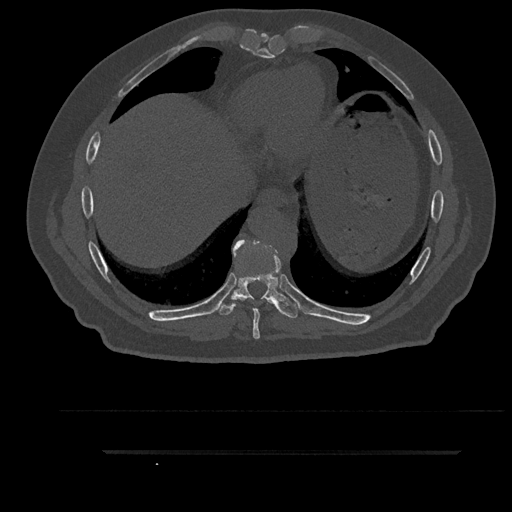
CT including the spine, one axial slice. Slice 444 of 797 in the series (ordered by position). Reconstruction kernel Br40s/3. Bone window (W 1800 / L 400 HU). 0.5 mm slice thickness. 512 × 512 image matrix, field of view 432 × 432 mm. Patient: male, 63 years. Case-level facts recorded for this patient, not image findings: primary cancer: renal; vertebrae with lytic lesions (as recorded): T8.
Annotated regions visible in this slice (semi-automatic segmentation, software-assisted and operator-edited):
- T8 vertebra: bounding box [x1, y1, x2, y2] px = [232, 240, 278, 339]
- T9 vertebra: [214, 241, 298, 318]